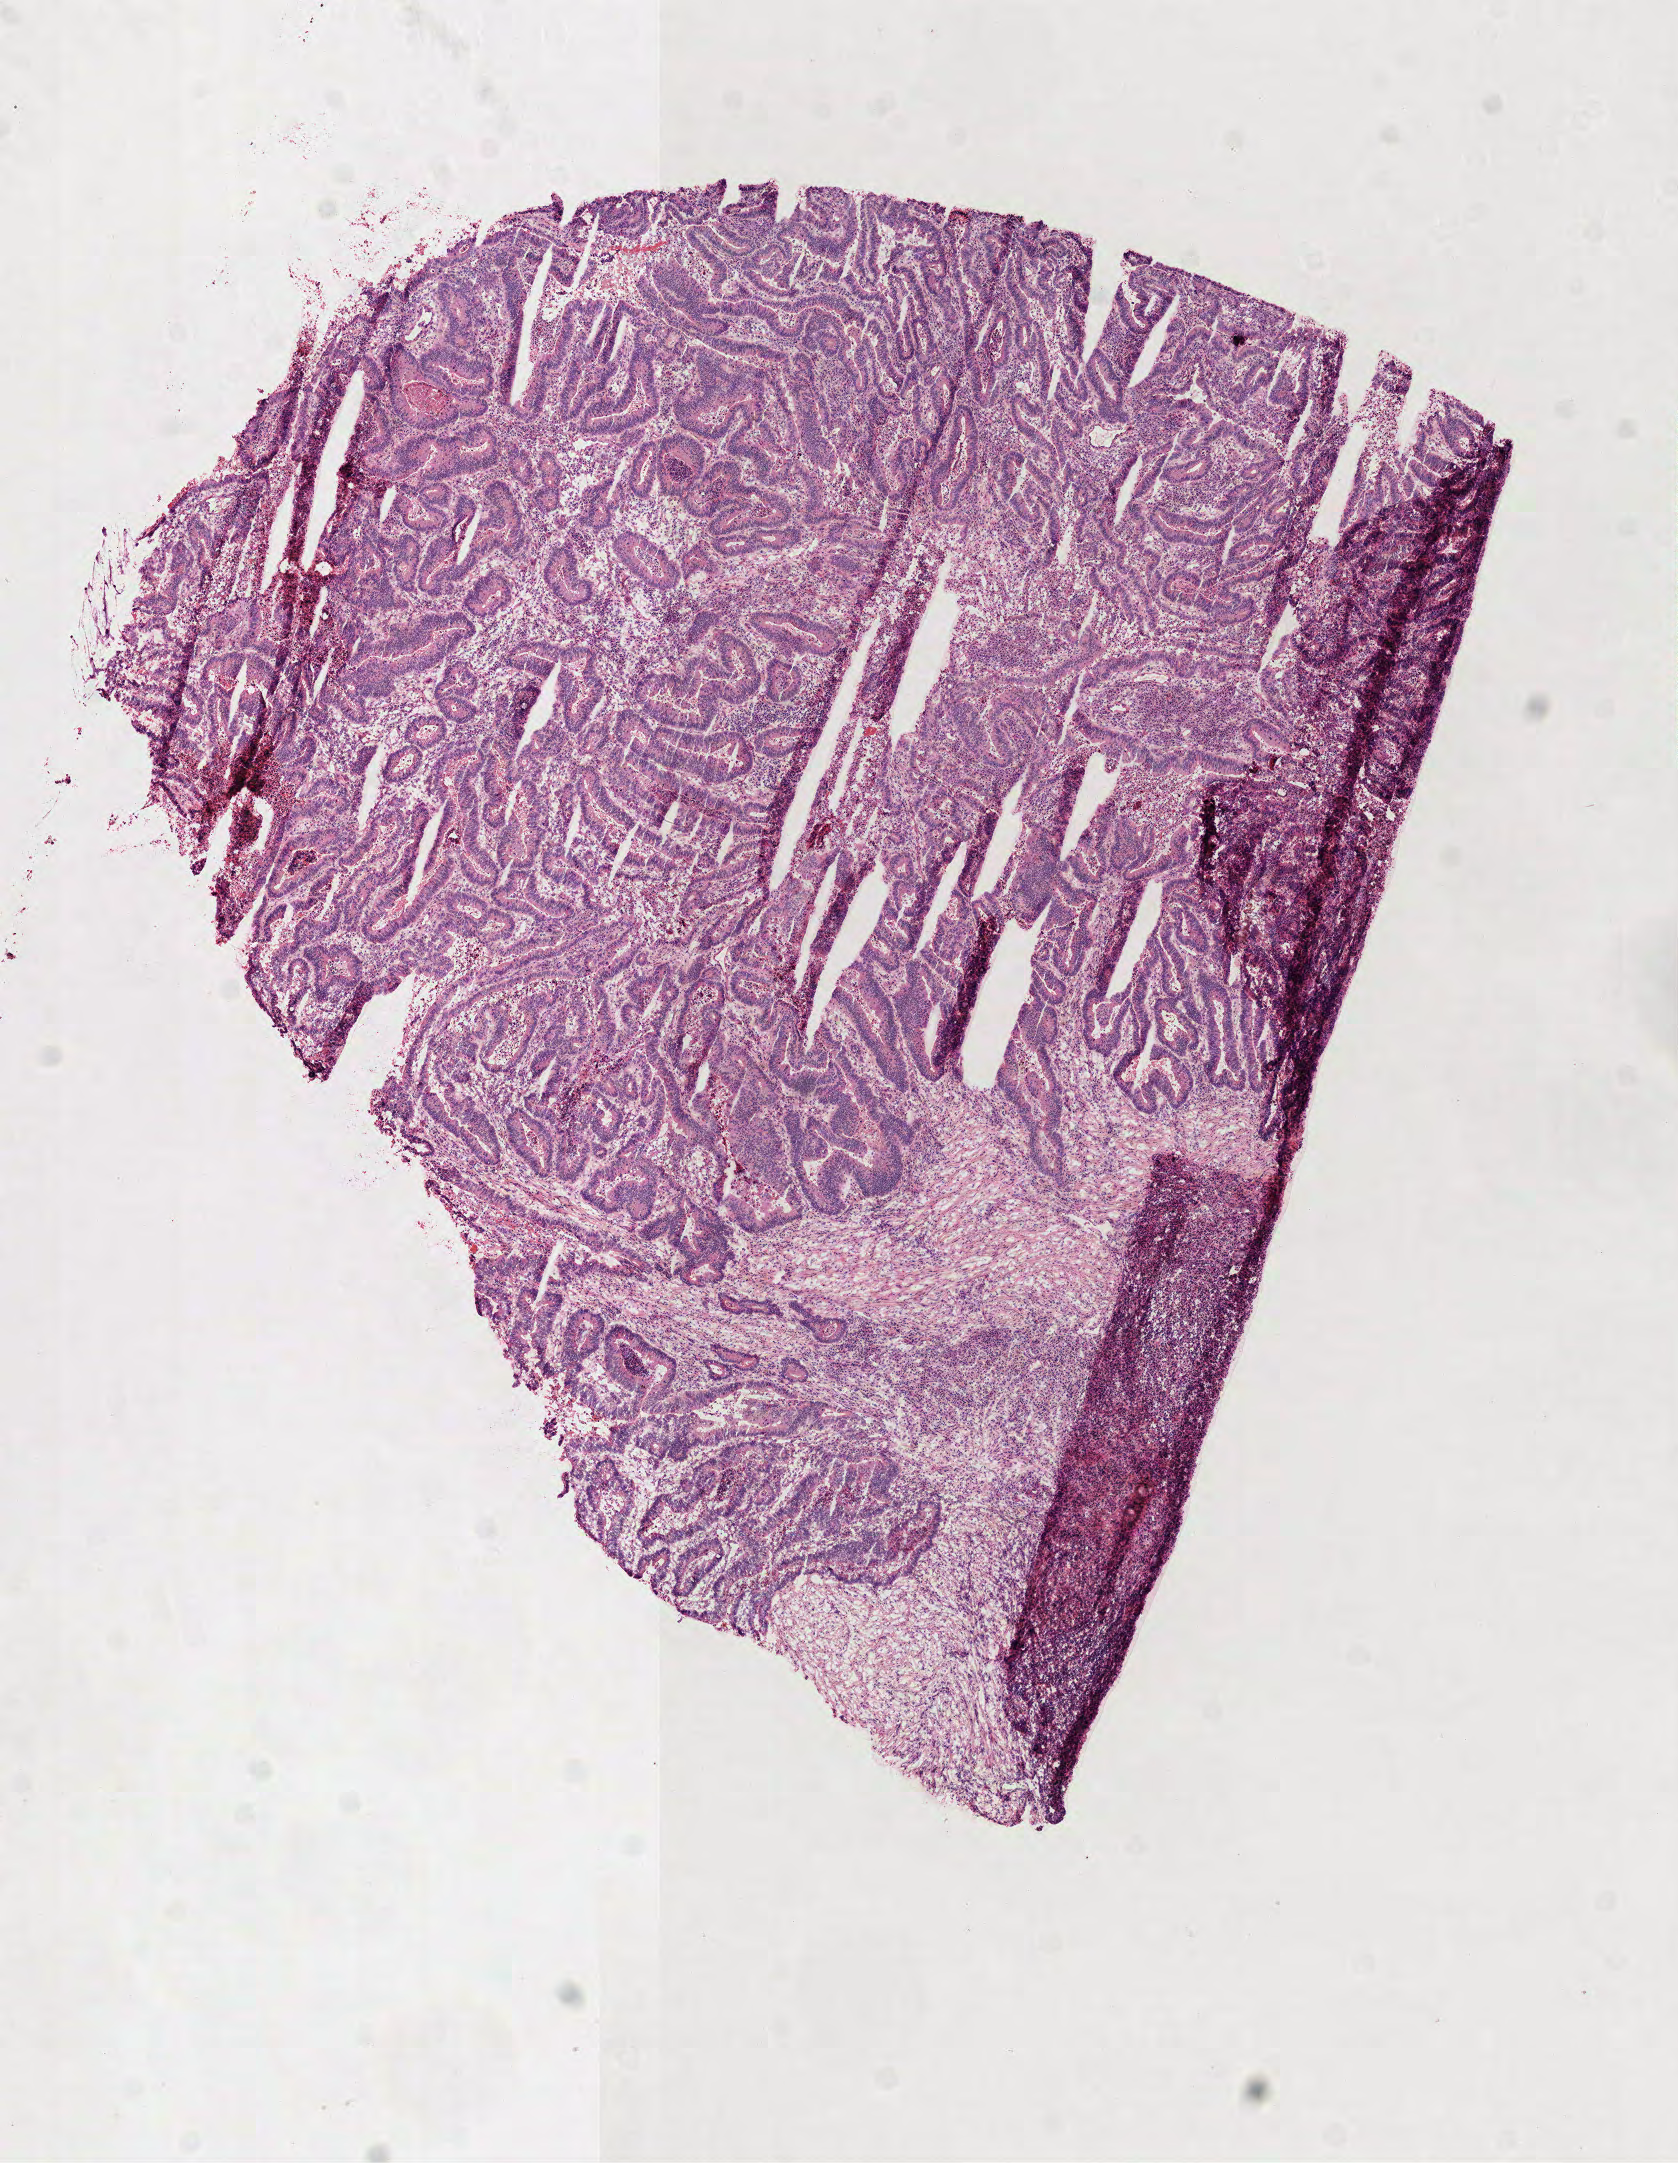
Digitized H&E-stained tissue section (whole slide), whole scanned area (about 6.8 x 8.7 mm) shown as a low-resolution overview; frozen section from the top of the tissue portion; rectum, primary tumour sample. Male, age 52 years at initial diagnosis. Composition of this section per pathologist review: tumour cells 75%, tumour nuclei 75%, normal cells 0%, stromal cells 20%, necrosis 5%.
* AJCC pathologic stage: IIIB
* lymph nodes positive (case pathology): 4 of 18 examined
* pathologic diagnosis: Adenocarcinoma in tubulovillous adenoma
* TNM: T3 N1 M0